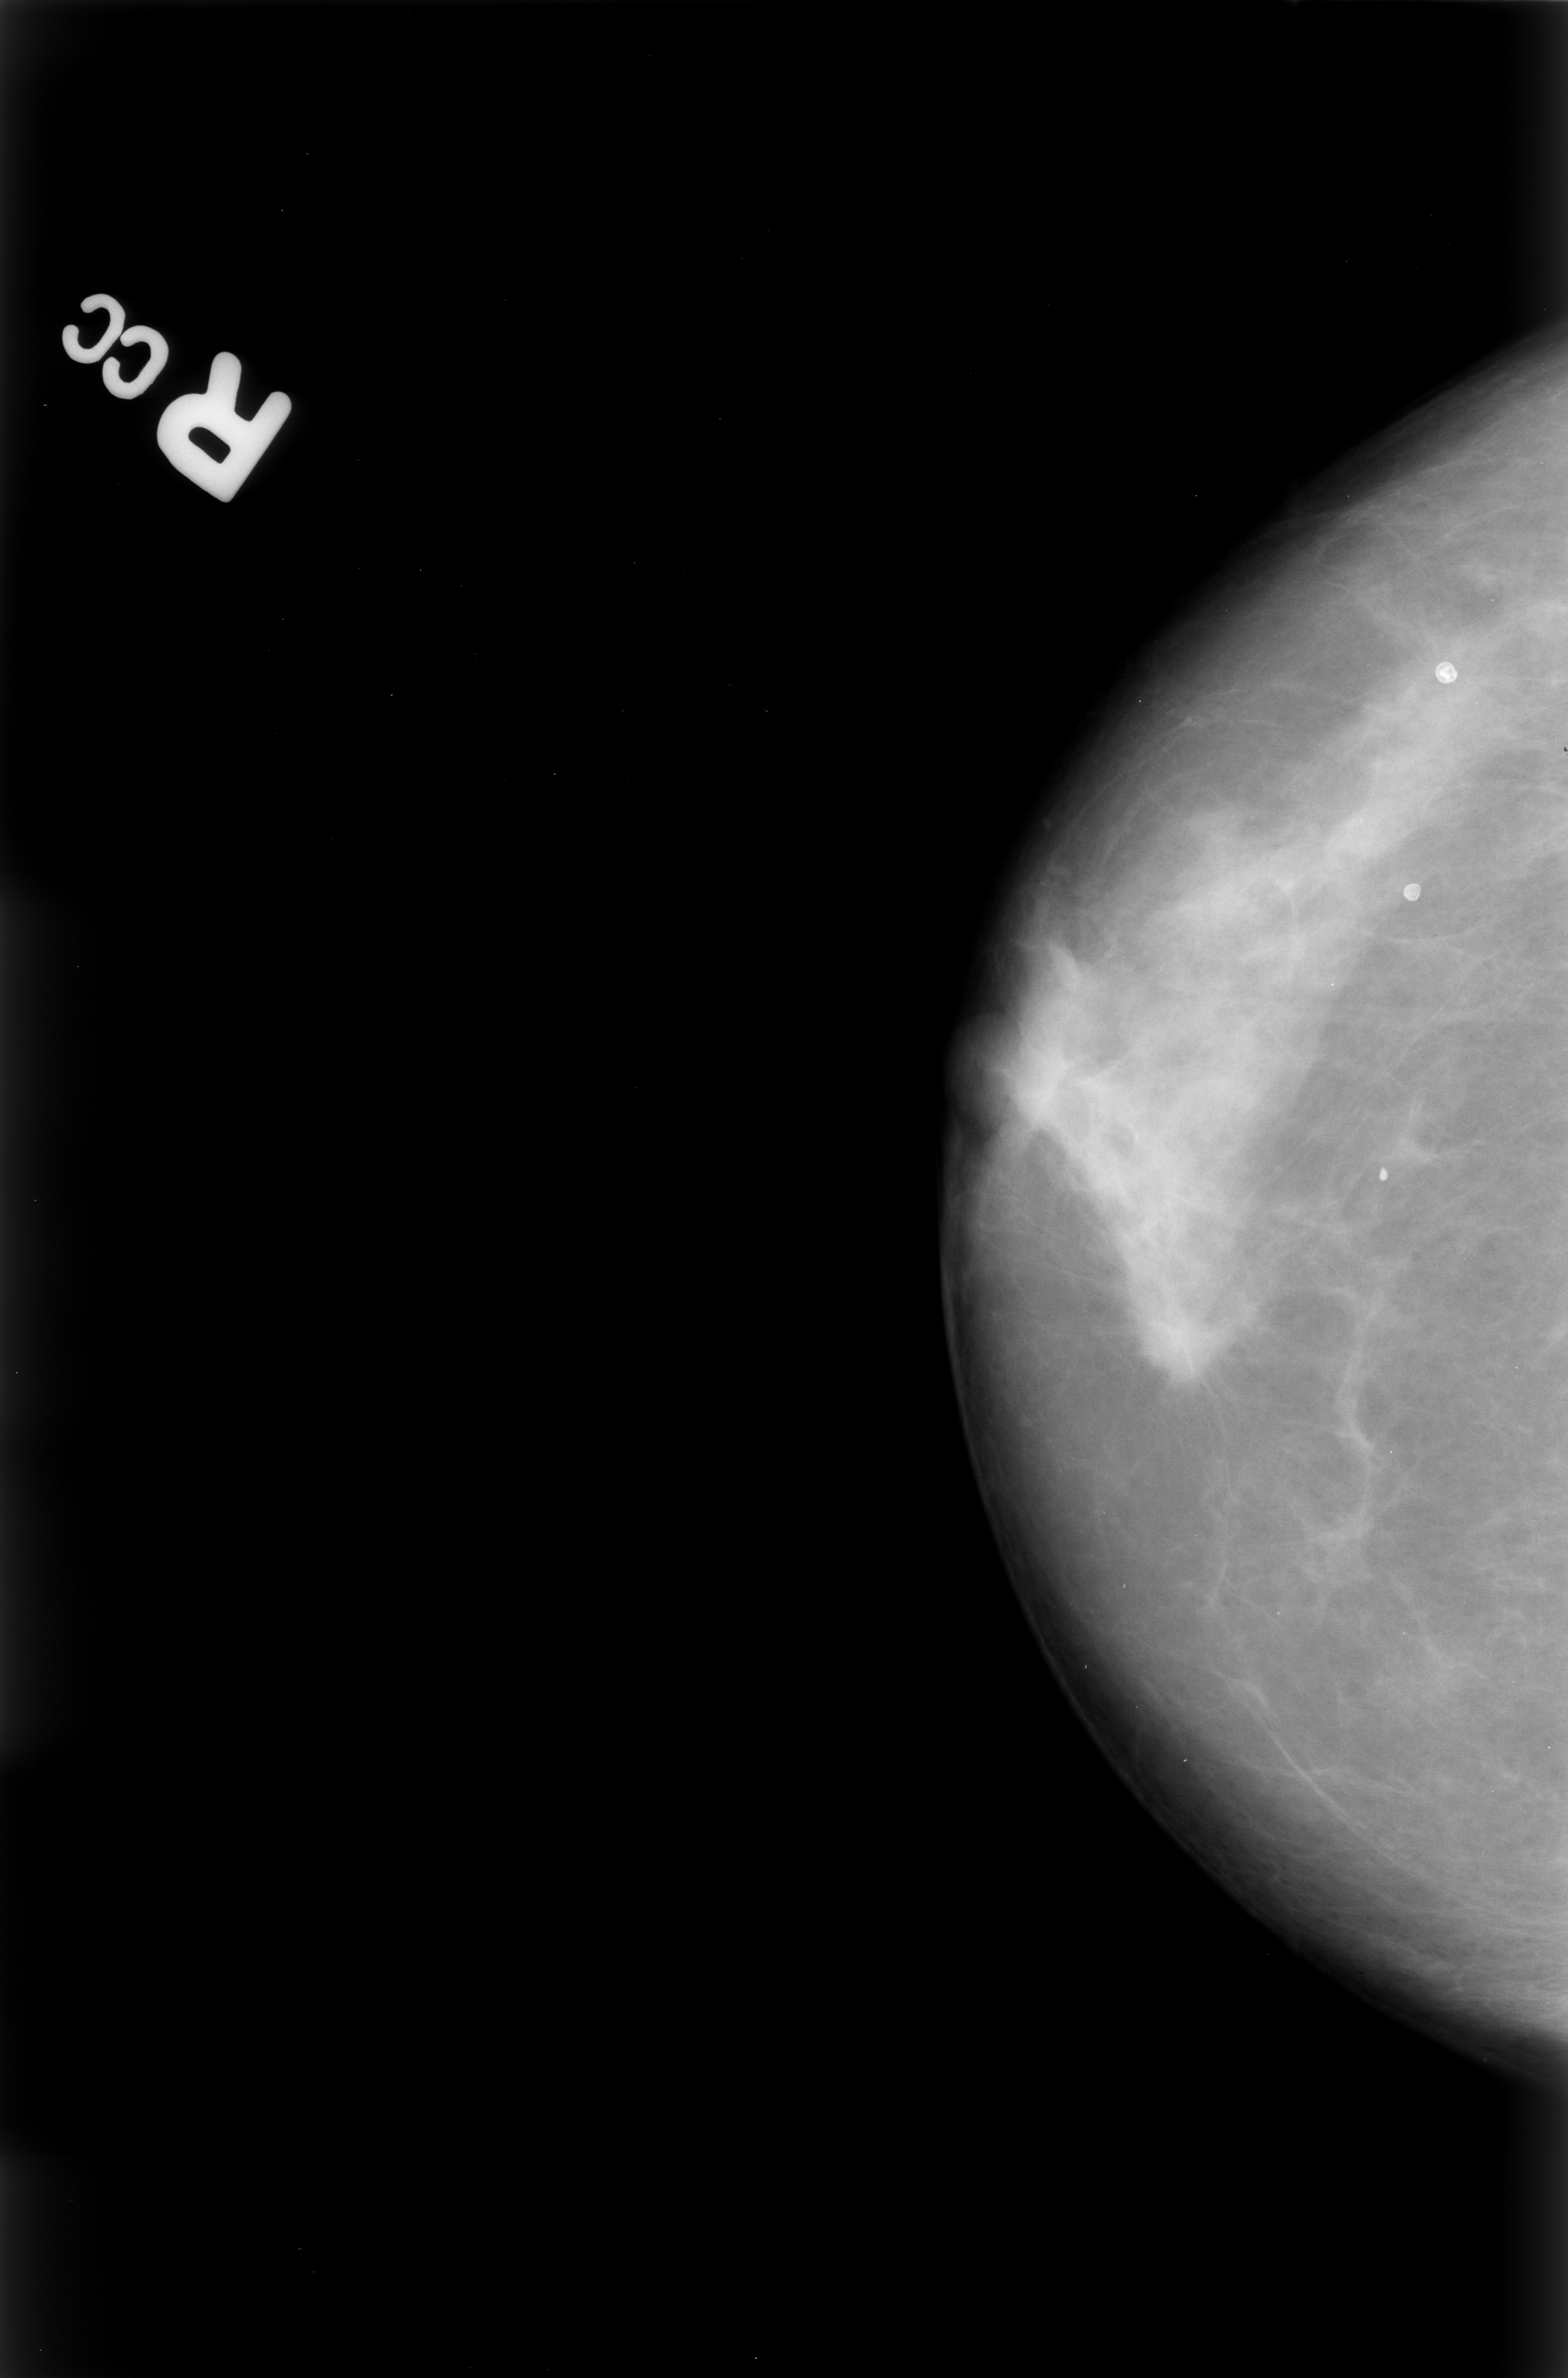
Digitized screen-film mammogram; right breast; CC view; breast composition: heterogeneously dense (BI-RADS density category 3 of 4); 1568 × 2378 image matrix.
Expert-marked regions of interest on this film, with their recorded descriptors:
- mass, shape irregular / architectural distortion, margins spiculated; BI-RADS assessment category 5; pathology result (as recorded, not read from the image): malignant: box from (x=1113, y=1244) to (x=1254, y=1389) px